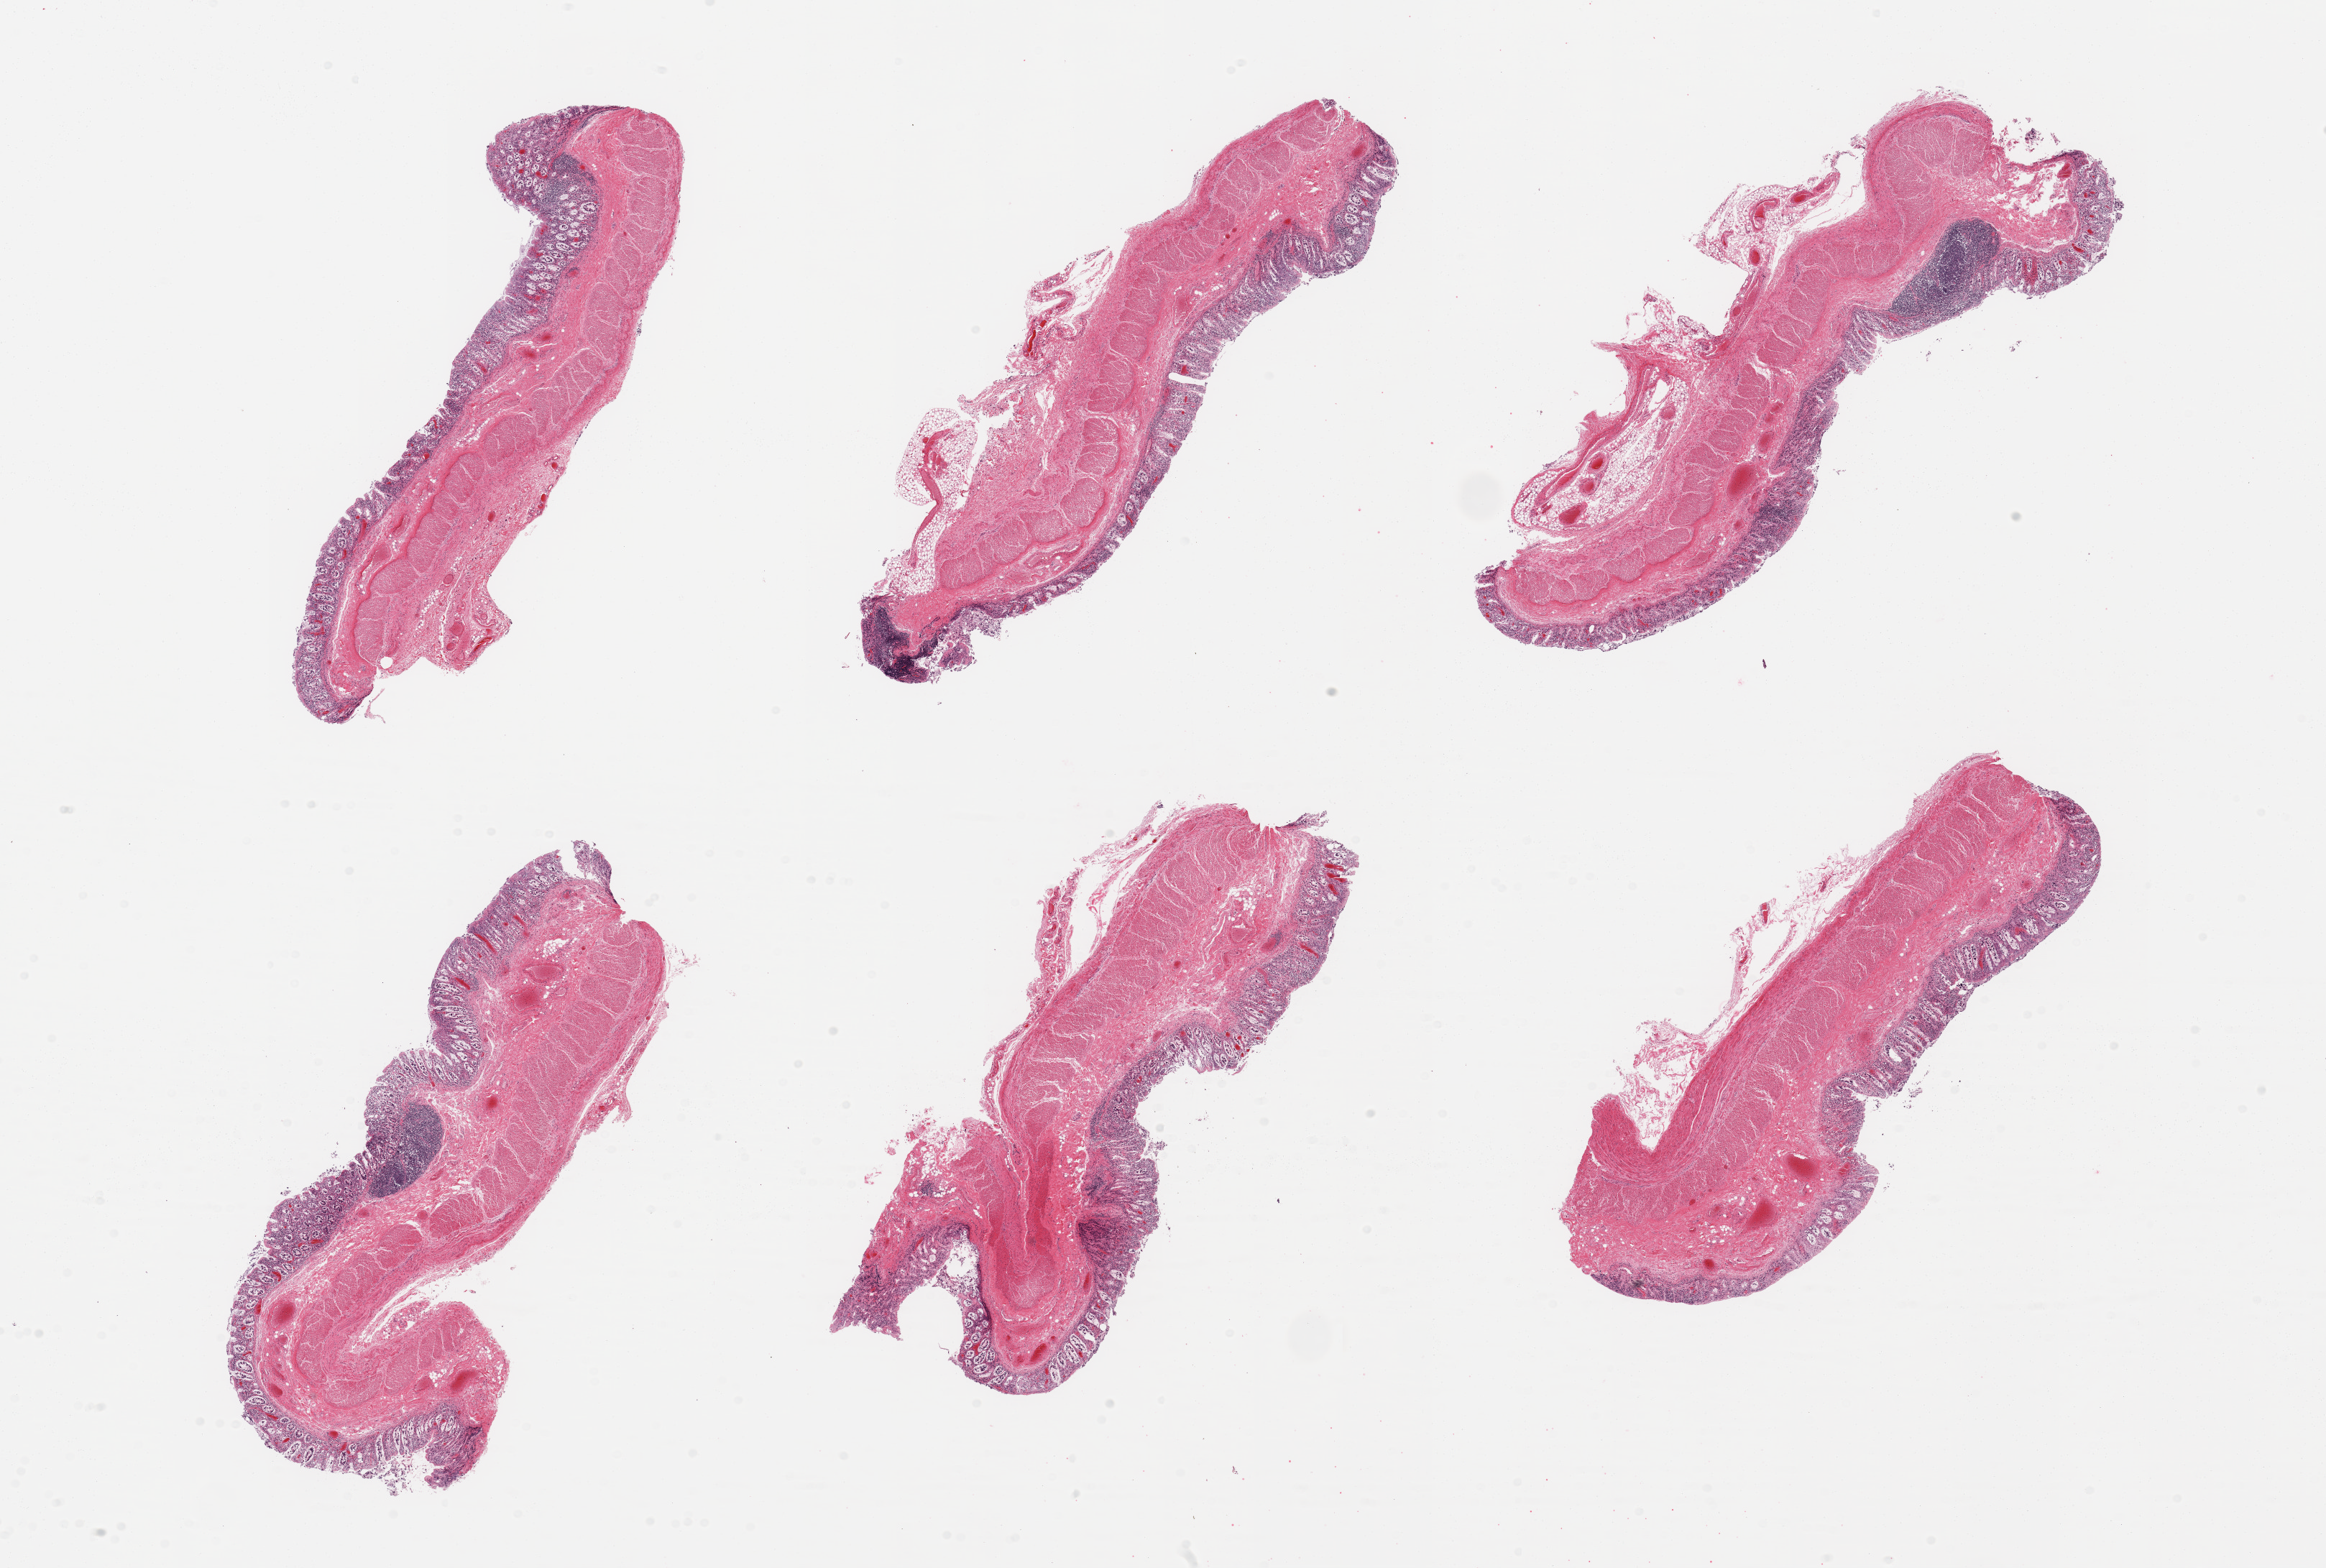
Hematoxylin and eosin (H&E) whole-slide image — a low-resolution overview of the entire scanned area, about 25.6 x 17.3 mm, PAXgene-fixed, paraffin-embedded tissue, section of transverse colon (target tissue), tissue donor sample. Donor sex: male.
* pathologist's review note for this sample: 6 pieces; moderate to severe mucosal autolysis; congestion; preserved muscularis; two lymphoid aggregates